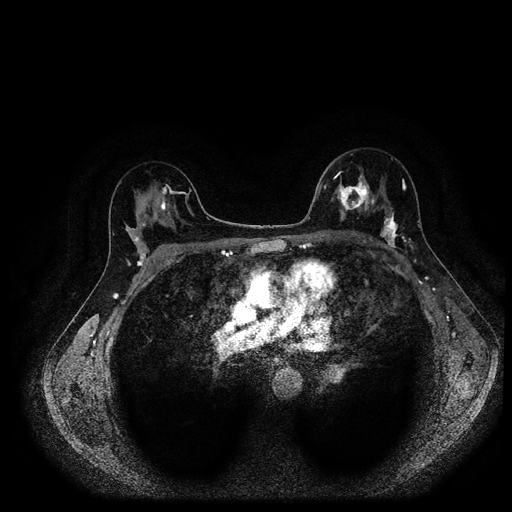
Breast MRI (dynamic contrast-enhanced, multi-phase), one axial slice. Slice 63 of 116 in the series (ordered by position). Dynamic contrast-enhanced series, time point 2 of 5 at this slice position (early post-contrast). 1.5 T. TE 2.7 ms, TR 5.4 ms. 2 mm slice thickness. 512 × 512 image matrix. Female patient, age 40 years.
Structures marked on this image (semi-automatic segmentation, software-assisted and operator-edited):
- breast lesion (labelled 'tumour' in the annotation; benign lesions carry a separate 'benign' label): box from (x=331, y=180) to (x=372, y=216) px